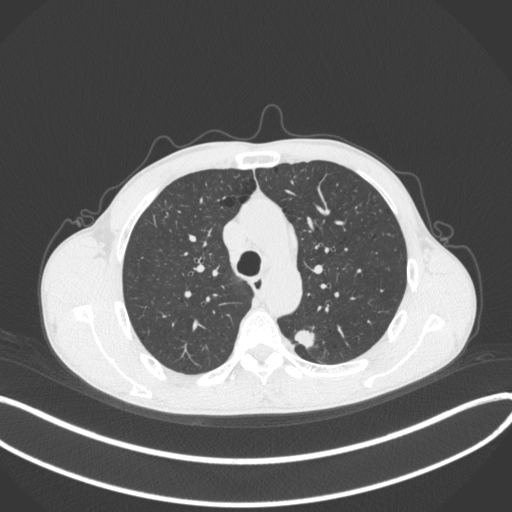
Chest CT, one axial slice. Slice 283 of 429 in the series (ordered by position). Reconstruction kernel B31f. 120 kVp. Lung window (W 1500 / L -600 HU). 512 × 512 image matrix, field of view 400 × 400 mm. Patient: male, 51 years. Case-level facts recorded for this patient, not image findings: clinical TNM (as recorded): T2a N1 M1.
Structures marked on this image (bounding box drawn by a radiologist):
- lung tumour (recorded histology: adenocarcinoma): box from (x=293, y=325) to (x=318, y=352) px